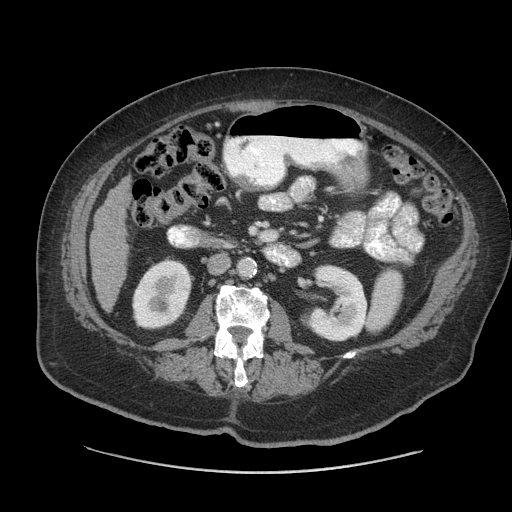
Contrast-enhanced abdominal CT (liver protocol), one axial slice. Position 17 of 91 along the scan axis. Reconstruction kernel STANDARD. 140 kVp. Soft-tissue window (W 400 / L 40 HU). 2.5 mm slice thickness. 512 × 512 image matrix, field of view 420 × 420 mm. From the clinical record (not read from this slice): diagnosis: hepatocellular carcinoma (patient treated with transarterial chemoembolisation; whether this scan precedes or follows treatment is not stated here); TNM stage (as recorded): Stage-I; Child-Pugh class: A; tumour differentiation: well differentiated; tumour nodularity: uninodular.
Structures marked on this image (semi-automatically segmented with operator editing):
- liver parenchyma outside the tumour (the mass and vessels are separate outlines, so this box may not span the whole liver): box from (x=90, y=177) to (x=130, y=310) px